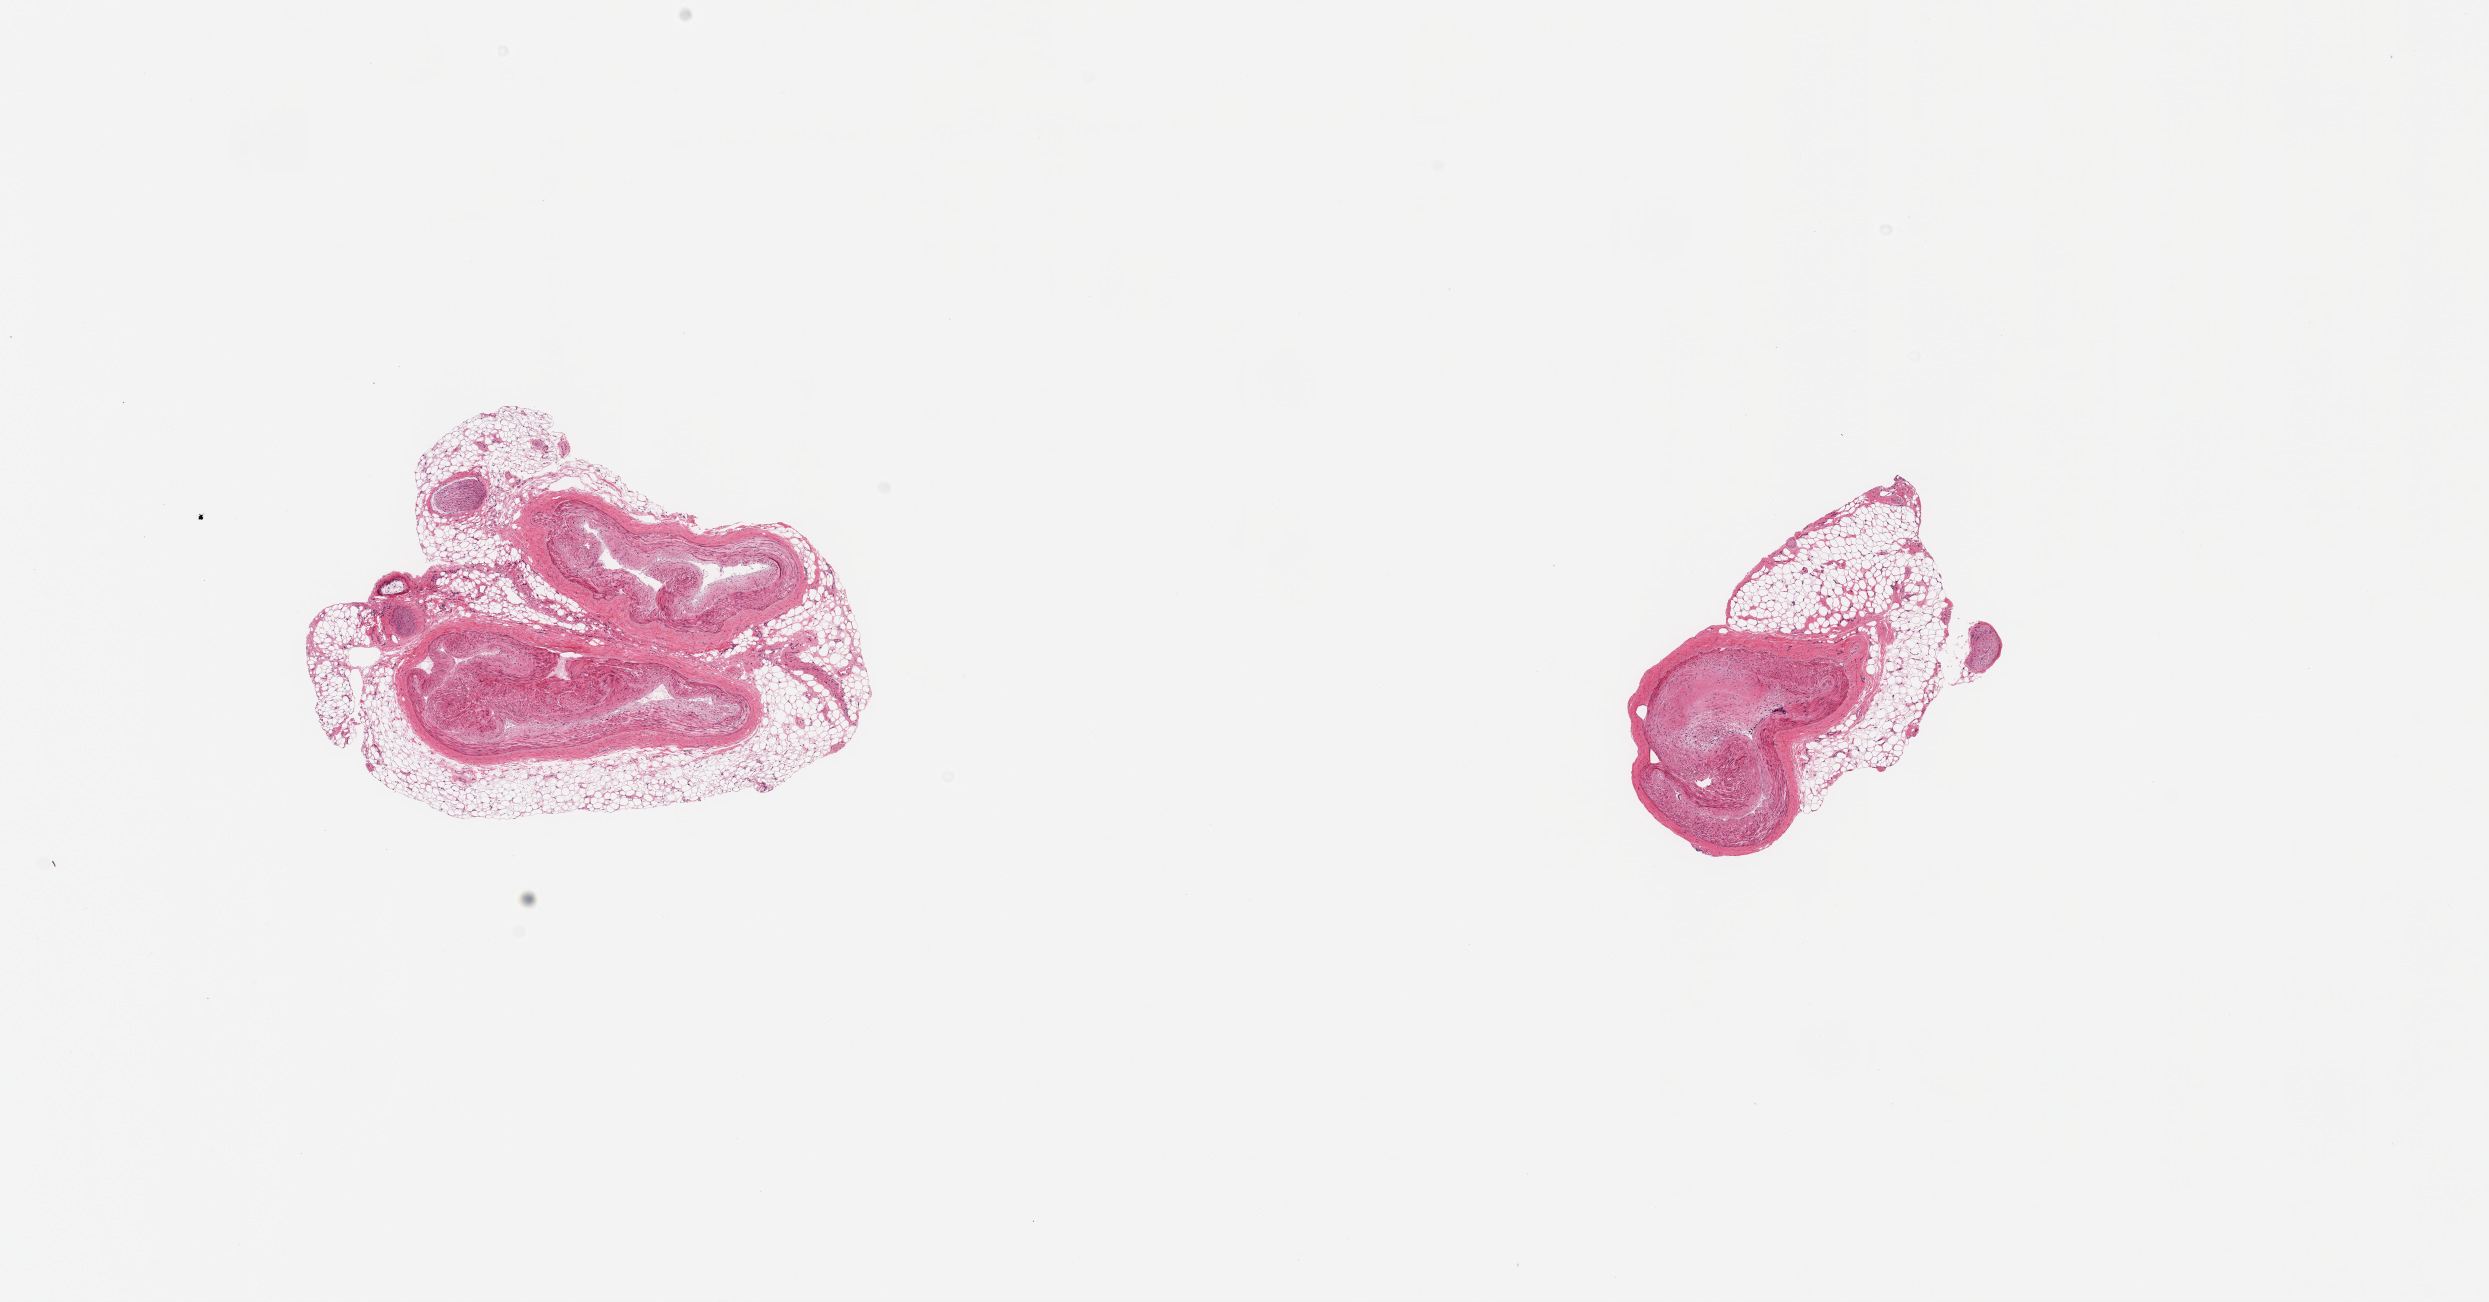
Whole-slide image, hematoxylin and eosin (H&E) stain, low-resolution overview of the scanned area, about 19.7 x 10.3 mm (slide scanned at 20x). PAXgene-fixed paraffin-embedded (PFPE) section. Sampled site (target tissue): coronary artery. Donor tissue sample. Donor: male.
- reviewer comment on this tissue sample: 2 pieces; sclerotic plaques; extraneous fat and nerve comprise 40% of samples